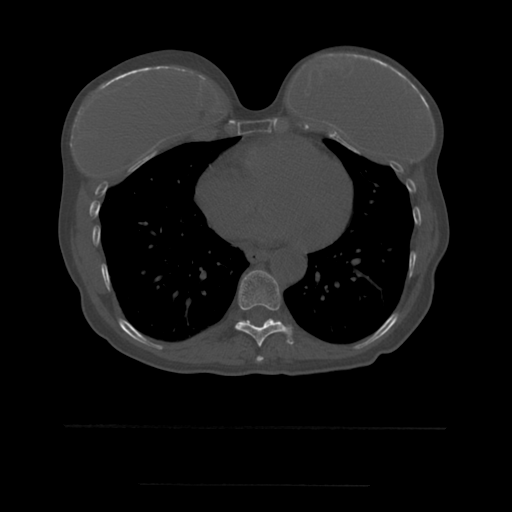
CT including the spine, one axial slice; slice 318 of 544 in the series (ordered by position); bone window (W 1800 / L 400 HU); 1.25 mm slice thickness; 512 × 512 image matrix, field of view 350 × 350 mm. Patient age 58 years. From the clinical record (not read from this slice): primary cancer: lung.
Structures marked on this image (semi-automatically segmented with operator editing):
- T8 vertebra: bounding box (x1, y1, x2, y2) in pixels: (257, 356, 264, 362)
- T9 vertebra: (236, 270, 294, 347)